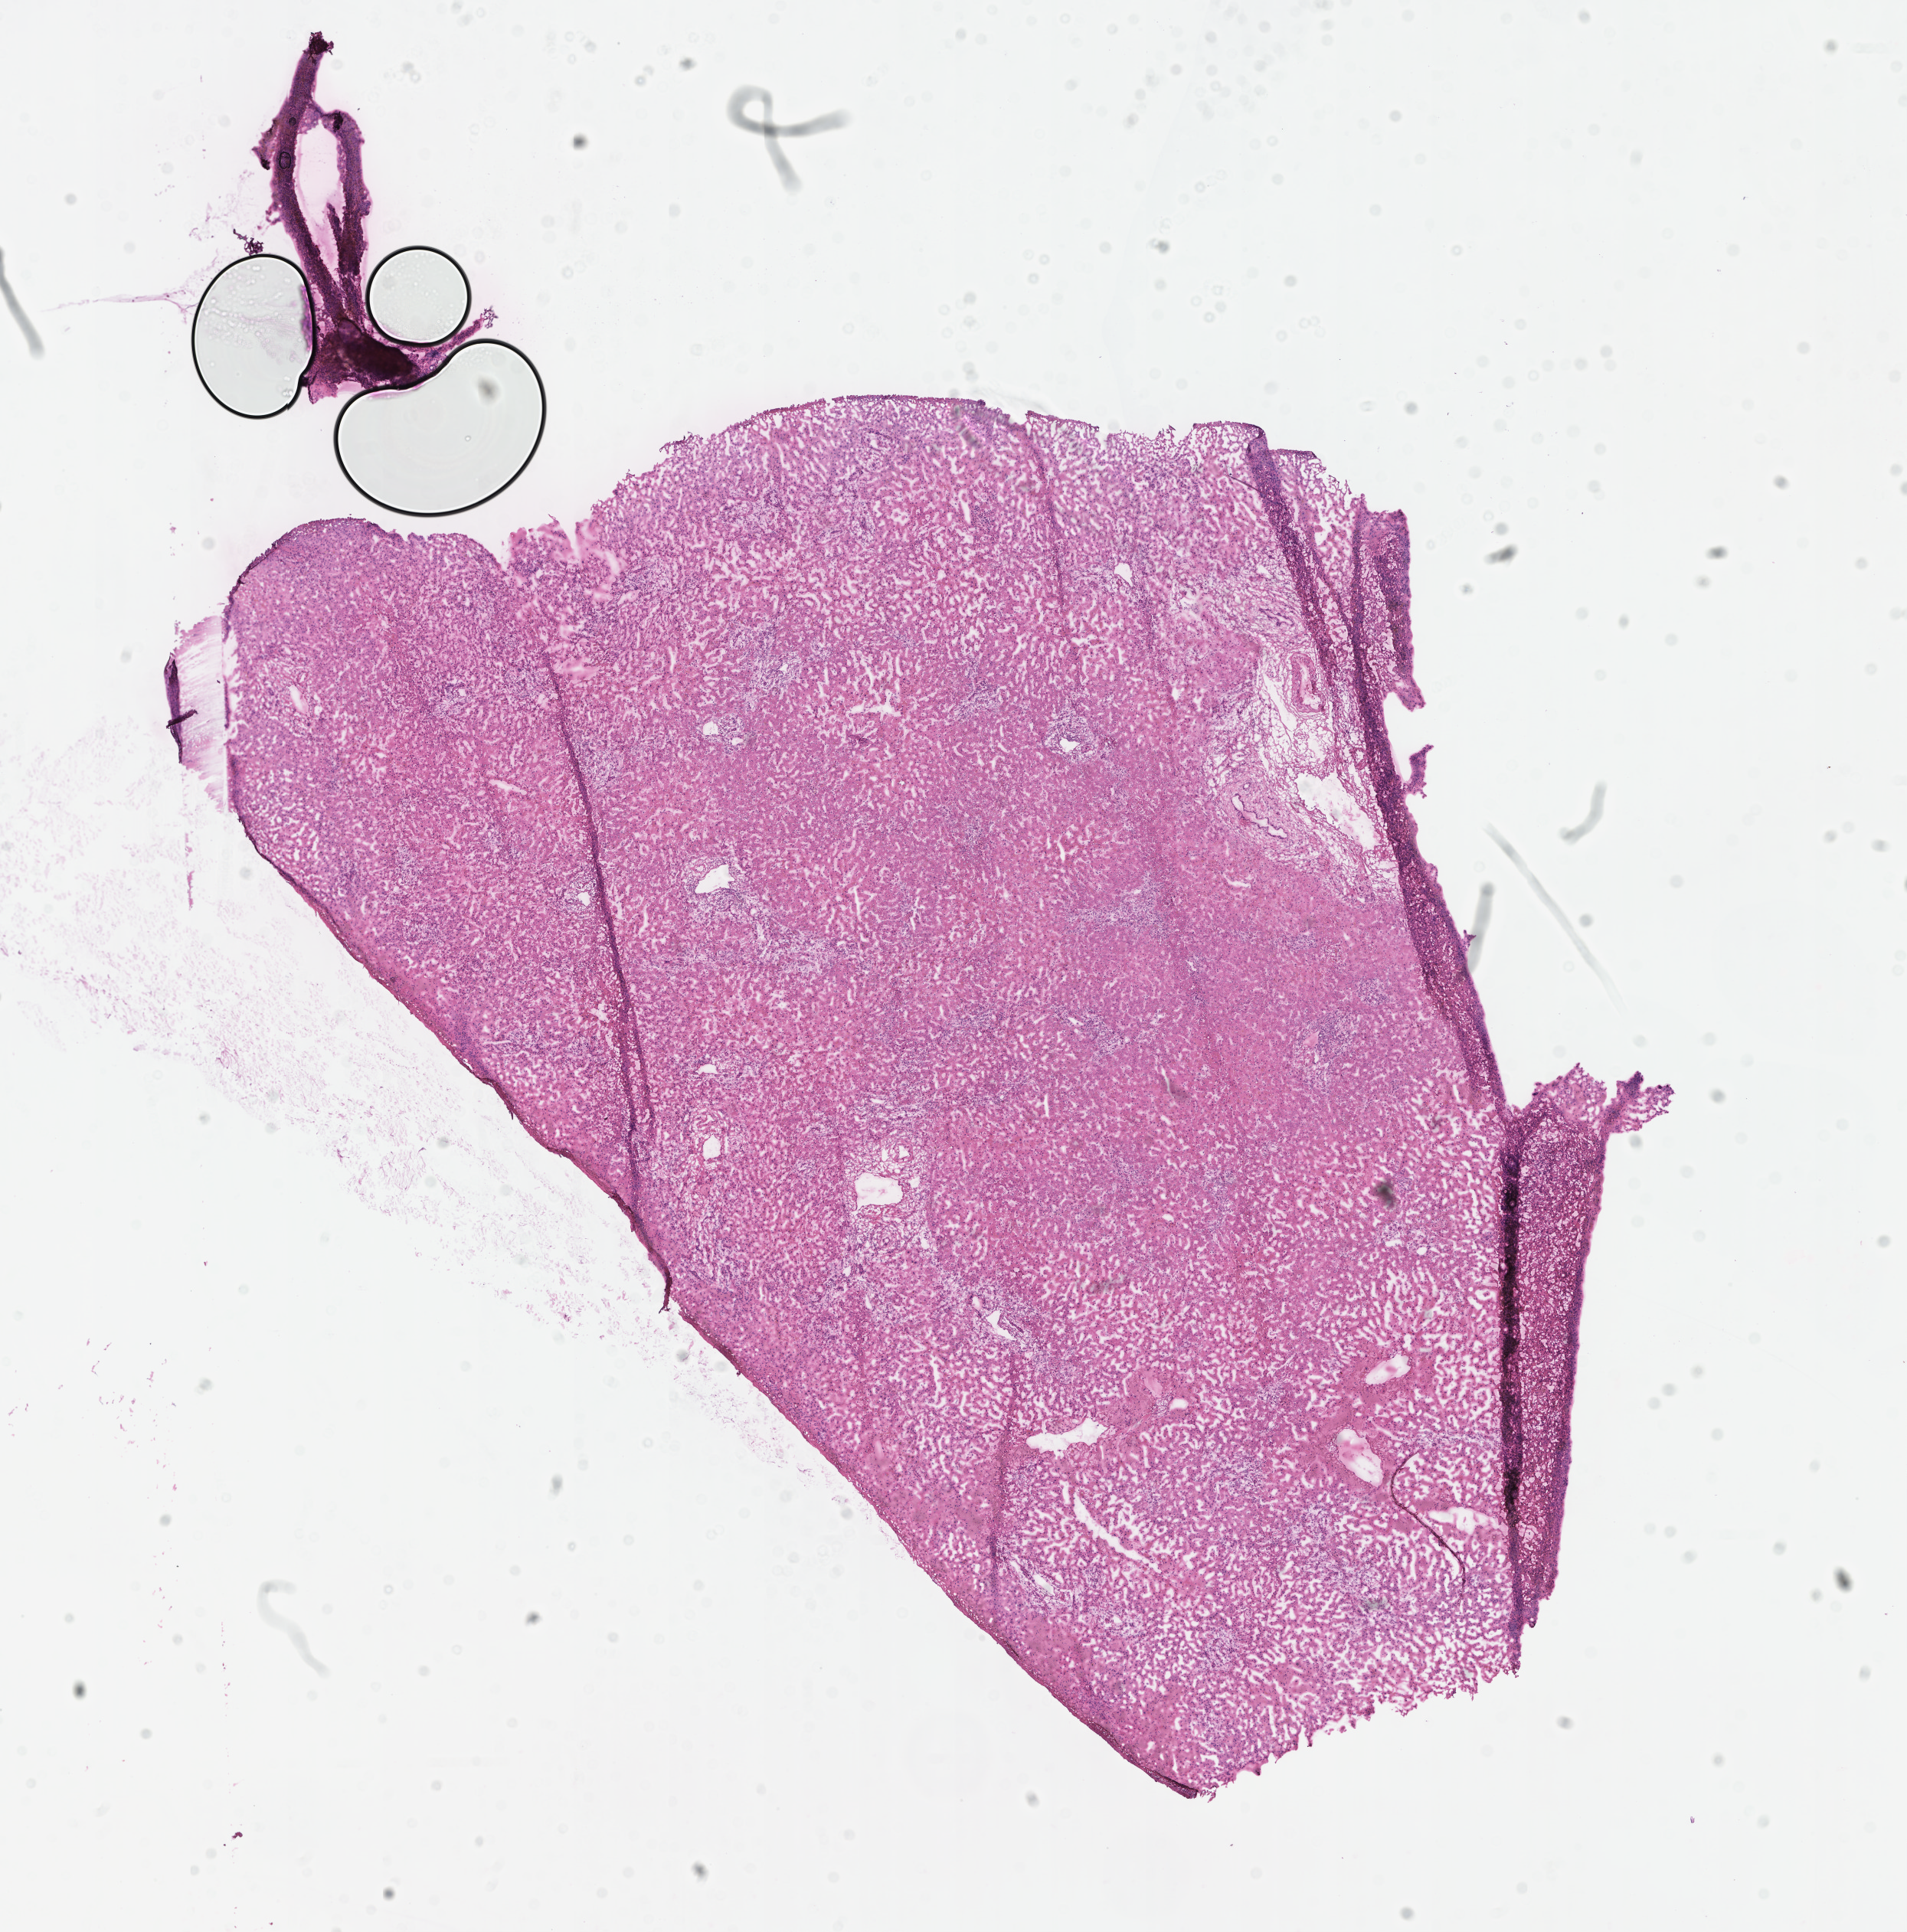
Whole-slide image, haematoxylin and eosin stain — low-resolution overview of the scanned area, about 10.1 x 10.2 mm, frozen section (tissue freezing medium), specimen: non-tumor (normal tissue) sample from a patient with adenocarcinoma, NOS, anatomic site: colon. Female patient; age at initial diagnosis 49 years. Slide review estimates, as recorded: tumor cells 0%, tumor nuclei 0%, stromal cells 0%, necrosis 0%, normal cells 100%. Infiltration values recorded for this section: lymphocyte infiltration 0%, monocyte infiltration 0%, neutrophil infiltration 0%.
This section: non-tumor tissue sample; the patient's diagnosis is given above. Section: bottom of the tissue portion.